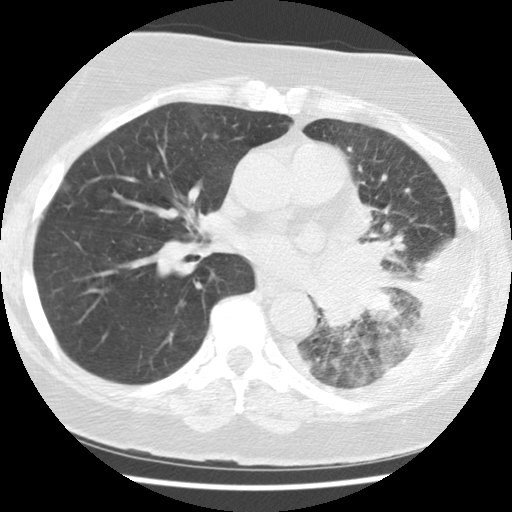
Chest CT (low-dose screening protocol), one axial image; baseline annual screen; lung window (W 1500 / L -600 HU); 2.5 mm slice thickness; standard (soft-tissue) reconstruction kernel (STANDARD); slice 58 of 114 in the series. Female participant, aged 65 years at enrolment.
Expert reader's lesion annotation, box from (x=301, y=282) to (x=405, y=365) px. Screening reader's record for this exam (one nodule recorded; not confirmed to be the boxed lesion): non-calcified nodule or mass ≥4 mm, left lower lobe, 74 × 48 mm, spiculated (stellate) margins, soft tissue attenuation. Lung cancer was diagnosed 13 days after this screen: adenocarcinoma, NOS, left lower lobe, stage IV (AJCC 6th edition), 74 mm at pathology.